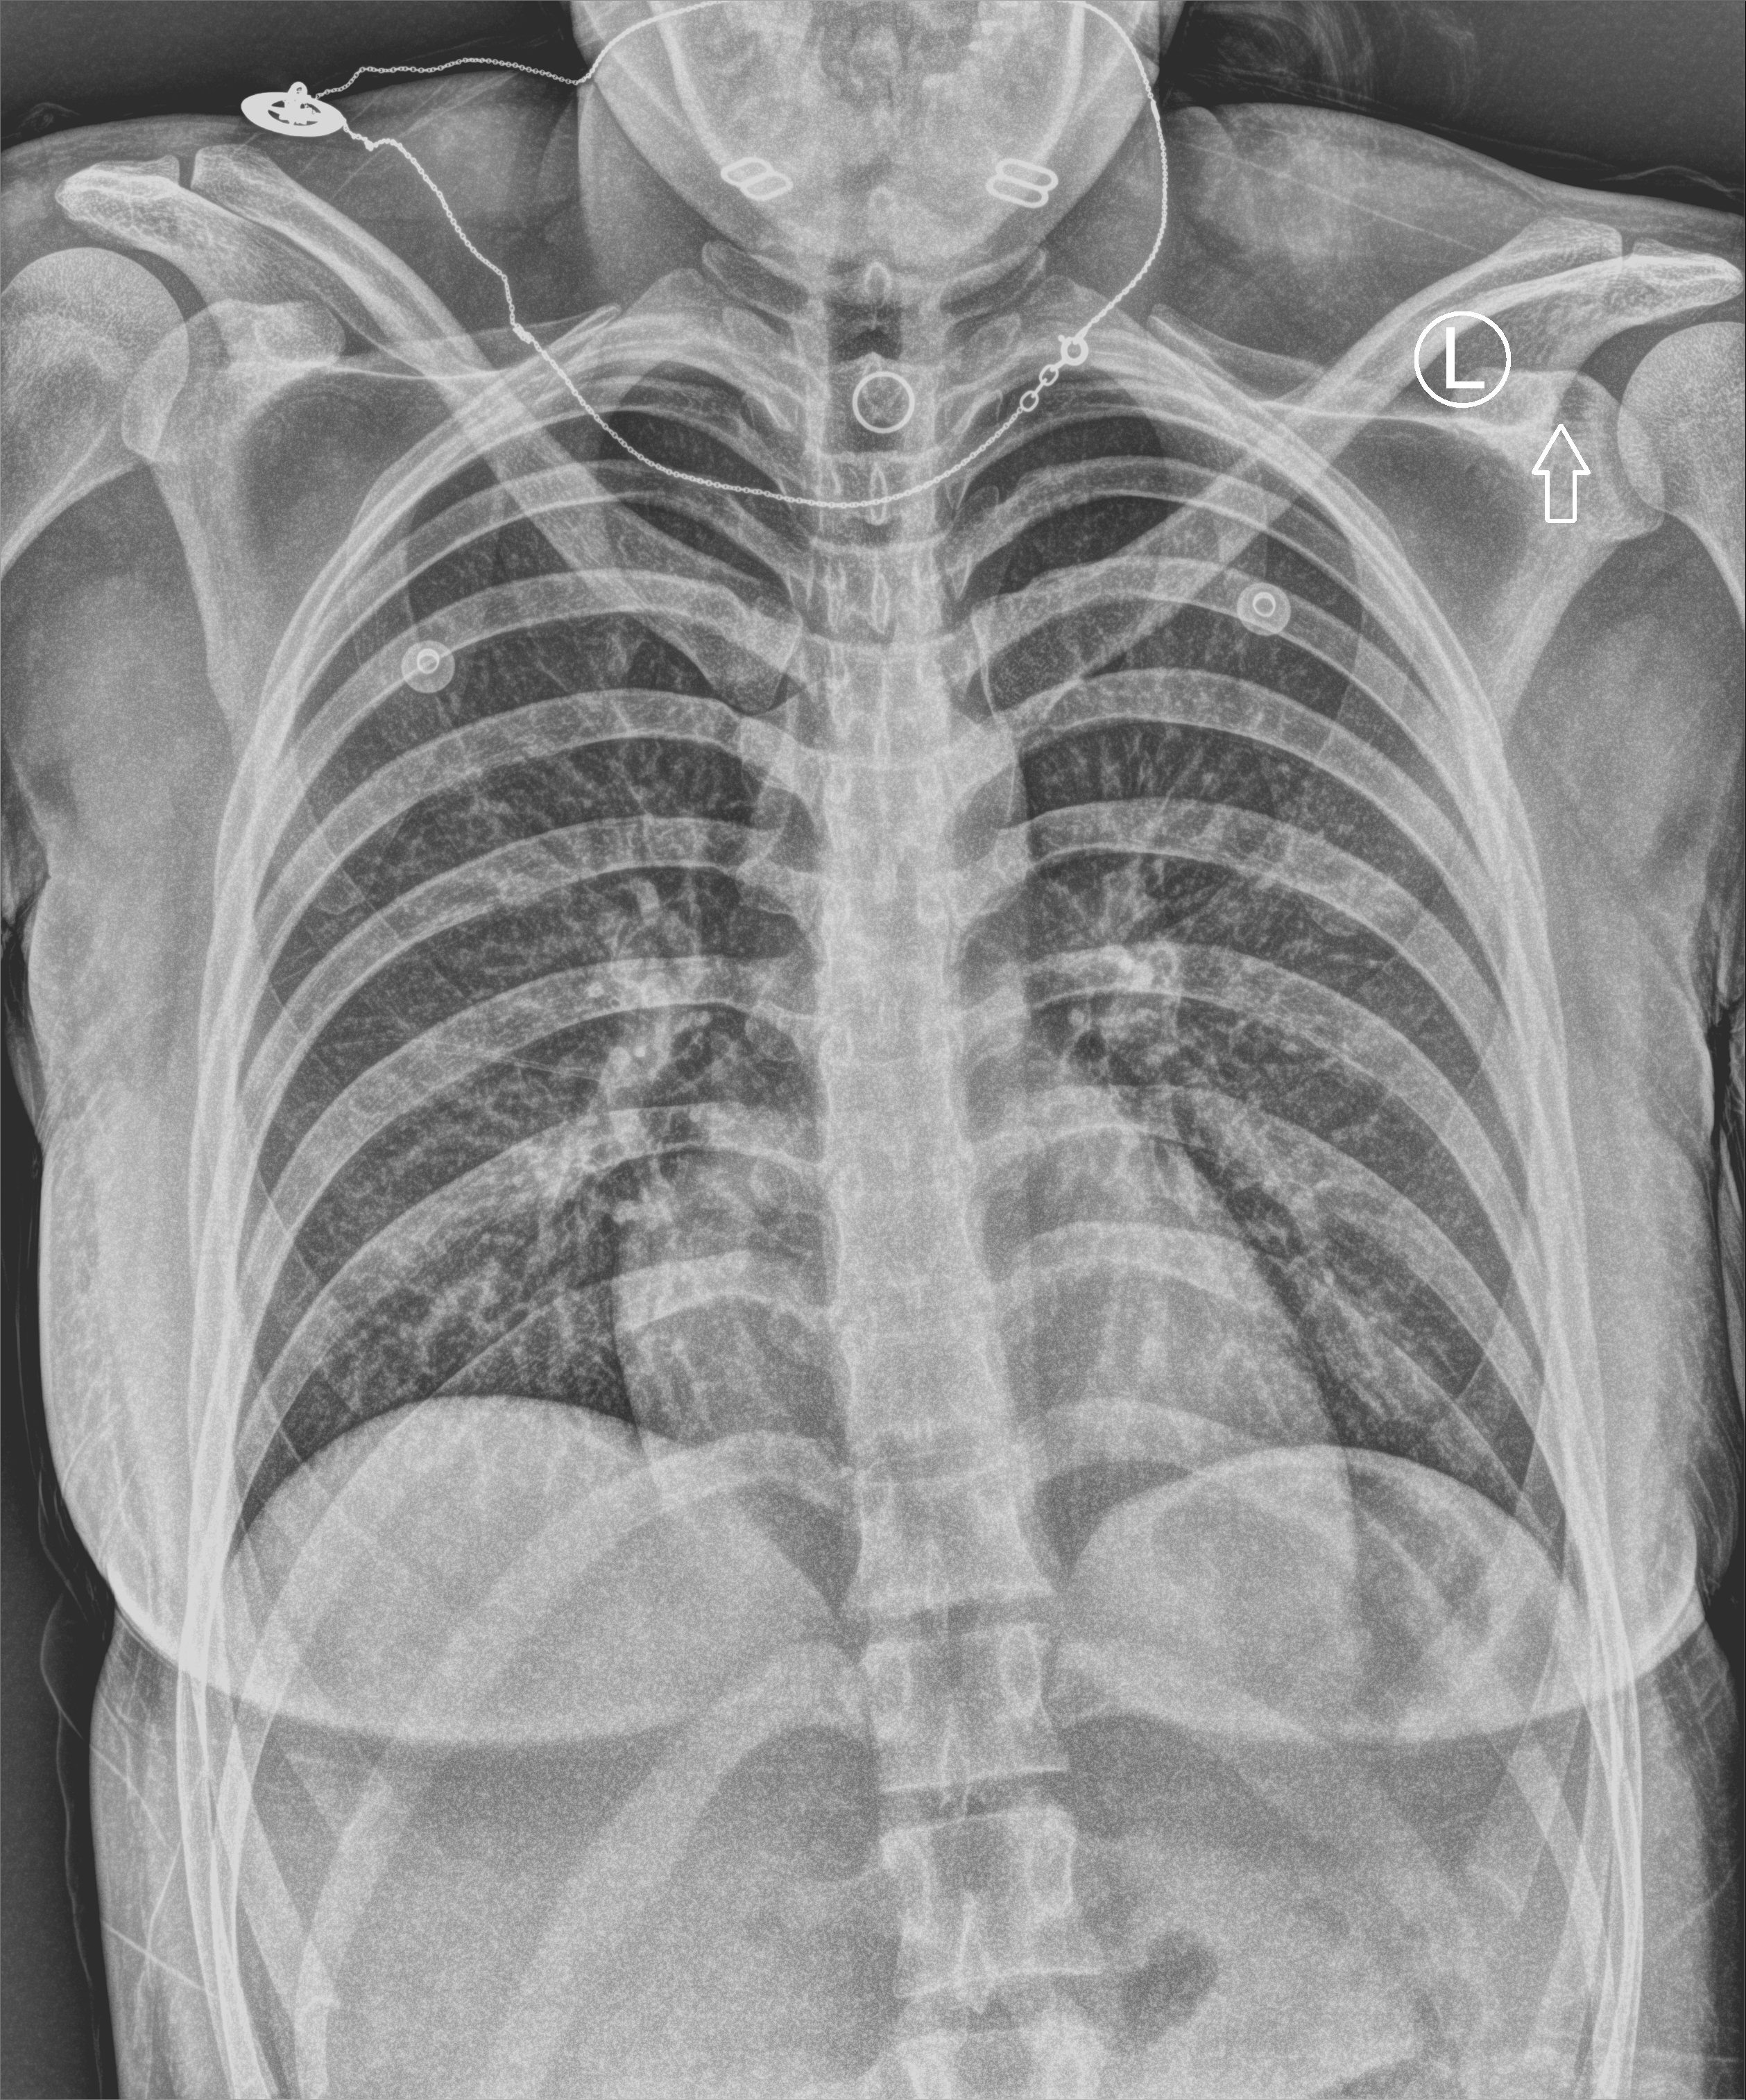
Bedside chest radiograph (computed radiography). Female patient hospitalised with COVID-19, age 18–59 years.
From the hospital-stay record, not from the radiograph (when in the stay this image was taken is not recorded):
- admitted to intensive care during this hospital stay: no
- length of hospital stay: 2 days